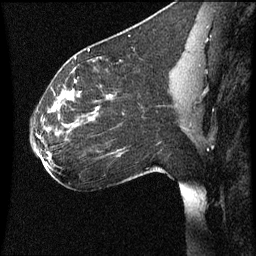
Breast MRI (dynamic contrast-enhanced), one sagittal slice; slice 35 of 60 in the series (ordered by position); dynamic contrast-enhanced series, image 2 of 3 at this slice position (ordered by acquisition); 1.5 T; TE 4.2 ms, TR 8.9 ms; 256 × 256 image matrix, field of view 200 × 200 mm. Patient: female, 35 years. From the clinical record (not read from this slice): setting: breast cancer imaged before/during neoadjuvant chemotherapy; receptor status: HER2-positive.
Annotated regions visible in this slice (semi-automatic segmentation, software-assisted and operator-edited):
- analysis volume of interest (the breast-tissue region the enhancement analysis was run in; not a lesion): bounding box (x1, y1, x2, y2) in pixels: (29, 66, 177, 177)
- tumour enhancement mask (voxels above the 70 % enhancement threshold inside the analysis volume of interest): (53, 90, 112, 113)